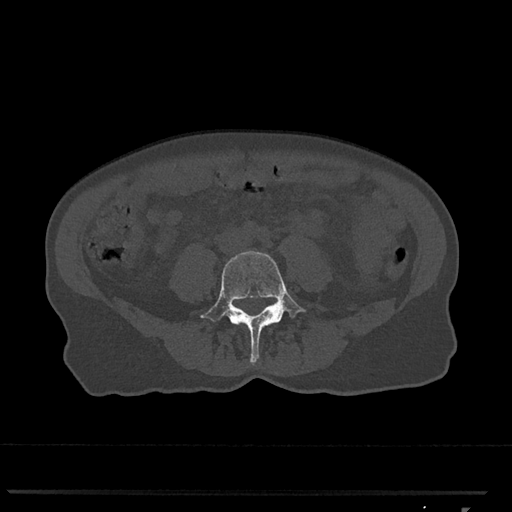
CT including the spine, one axial slice. Slice 211 of 793 in the series (ordered by position). Reconstruction kernel Br40s/3. 120 kVp. Bone window (W 1800 / L 400 HU). 512 × 512 image matrix, field of view 380 × 380 mm. Female patient, age 62 years. From the clinical record (not read from this slice): primary cancer: renal.
Structures marked on this image (semi-automatically segmented with operator editing):
- L4 vertebra: bounding box [x1, y1, x2, y2] px = [200, 250, 306, 365]